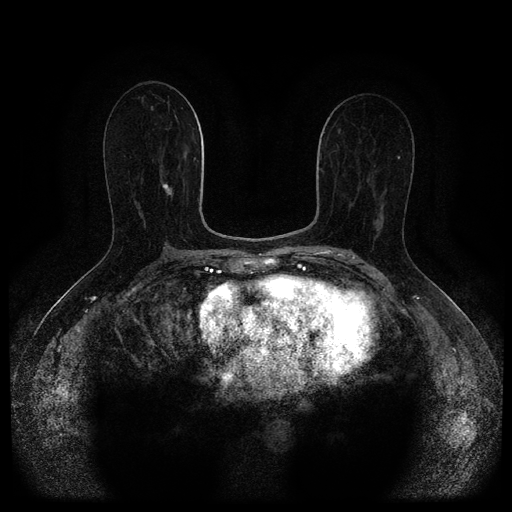
Breast MRI (dynamic contrast-enhanced, multi-phase), one axial slice. Slice 54 of 116 in the series (ordered by position). Dynamic contrast-enhanced series, time point 2 of 5 at this slice position (early post-contrast). 1.5 T. TE 2.7 ms, TR 5.4 ms. 2 mm slice thickness. 512 × 512 image matrix, field of view 340 × 340 mm. Patient: female, 71 years.
Annotated regions visible in this slice (semi-automatic segmentation, software-assisted and operator-edited):
- breast lesion (labelled 'tumour' in the annotation; benign lesions carry a separate 'benign' label): box from (x=162, y=183) to (x=173, y=195) px